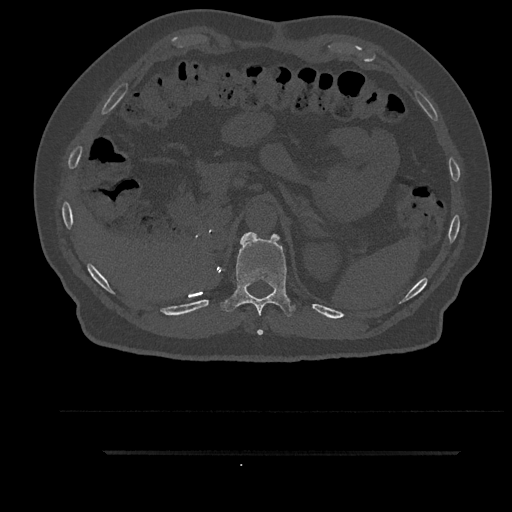
CT including the spine, one axial slice; position 303 of 797 along the scan axis; reconstruction kernel Br40s/3; bone window (W 1800 / L 400 HU); 512 × 512 image matrix. Male patient, age 63 years. Case-level facts recorded for this patient, not image findings: primary cancer: renal; vertebrae with lytic lesions (as recorded): T8.
Annotated regions visible in this slice (semi-automatically segmented with operator editing):
- T11 vertebra: bounding box [x1, y1, x2, y2] px = [220, 232, 296, 335]